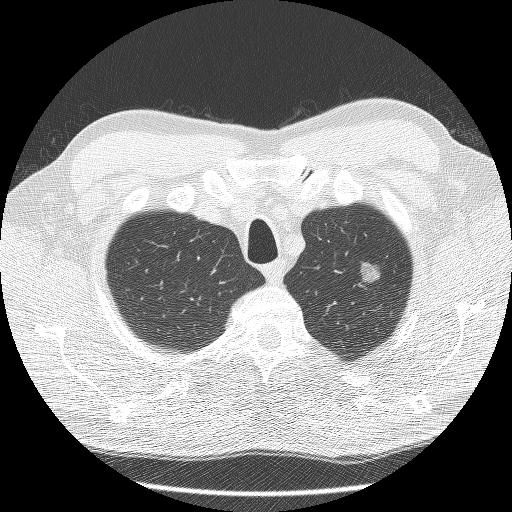
Low-dose screening chest CT, axial slice. Third screening round (two years after baseline). Lung window (W 1500 / L -600 HU). Lung (sharp) reconstruction kernel (BONE). Male participant, aged 60 years at enrolment. Former smoker at enrolment.
Expert-annotated lung lesion, bounding box [x1, y1, x2, y2] px = [336, 252, 393, 300]. The screening reader recorded 2 non-calcified nodules or masses ≥4 mm on this exam (right lower lobe, left upper lobe); which of them this box marks is not recorded. Official screen result: positive, other. Participant outcome: lung cancer diagnosed 99 days after this screen — bronchiolo-alveolar carcinoma, non-mucinous, left upper lobe, well differentiated (G1), stage IA (AJCC 6th edition), 16 mm at pathology.